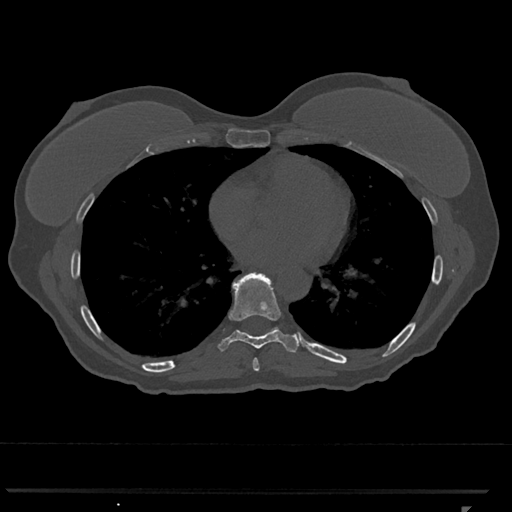
CT including the spine, one axial slice; slice 662 of 793 in the series (ordered by position); reconstruction kernel Br40s/3; 120 kVp; bone window (W 1800 / L 400 HU); 512 × 512 image matrix, field of view 380 × 380 mm. Female patient, age 62 years. From the clinical record (not read from this slice): primary cancer: renal.
Outlined on this slice (semi-automatically segmented with operator editing):
- T7 vertebra: bounding box [x1, y1, x2, y2] px = [253, 358, 260, 371]
- T8 vertebra: [218, 273, 300, 353]